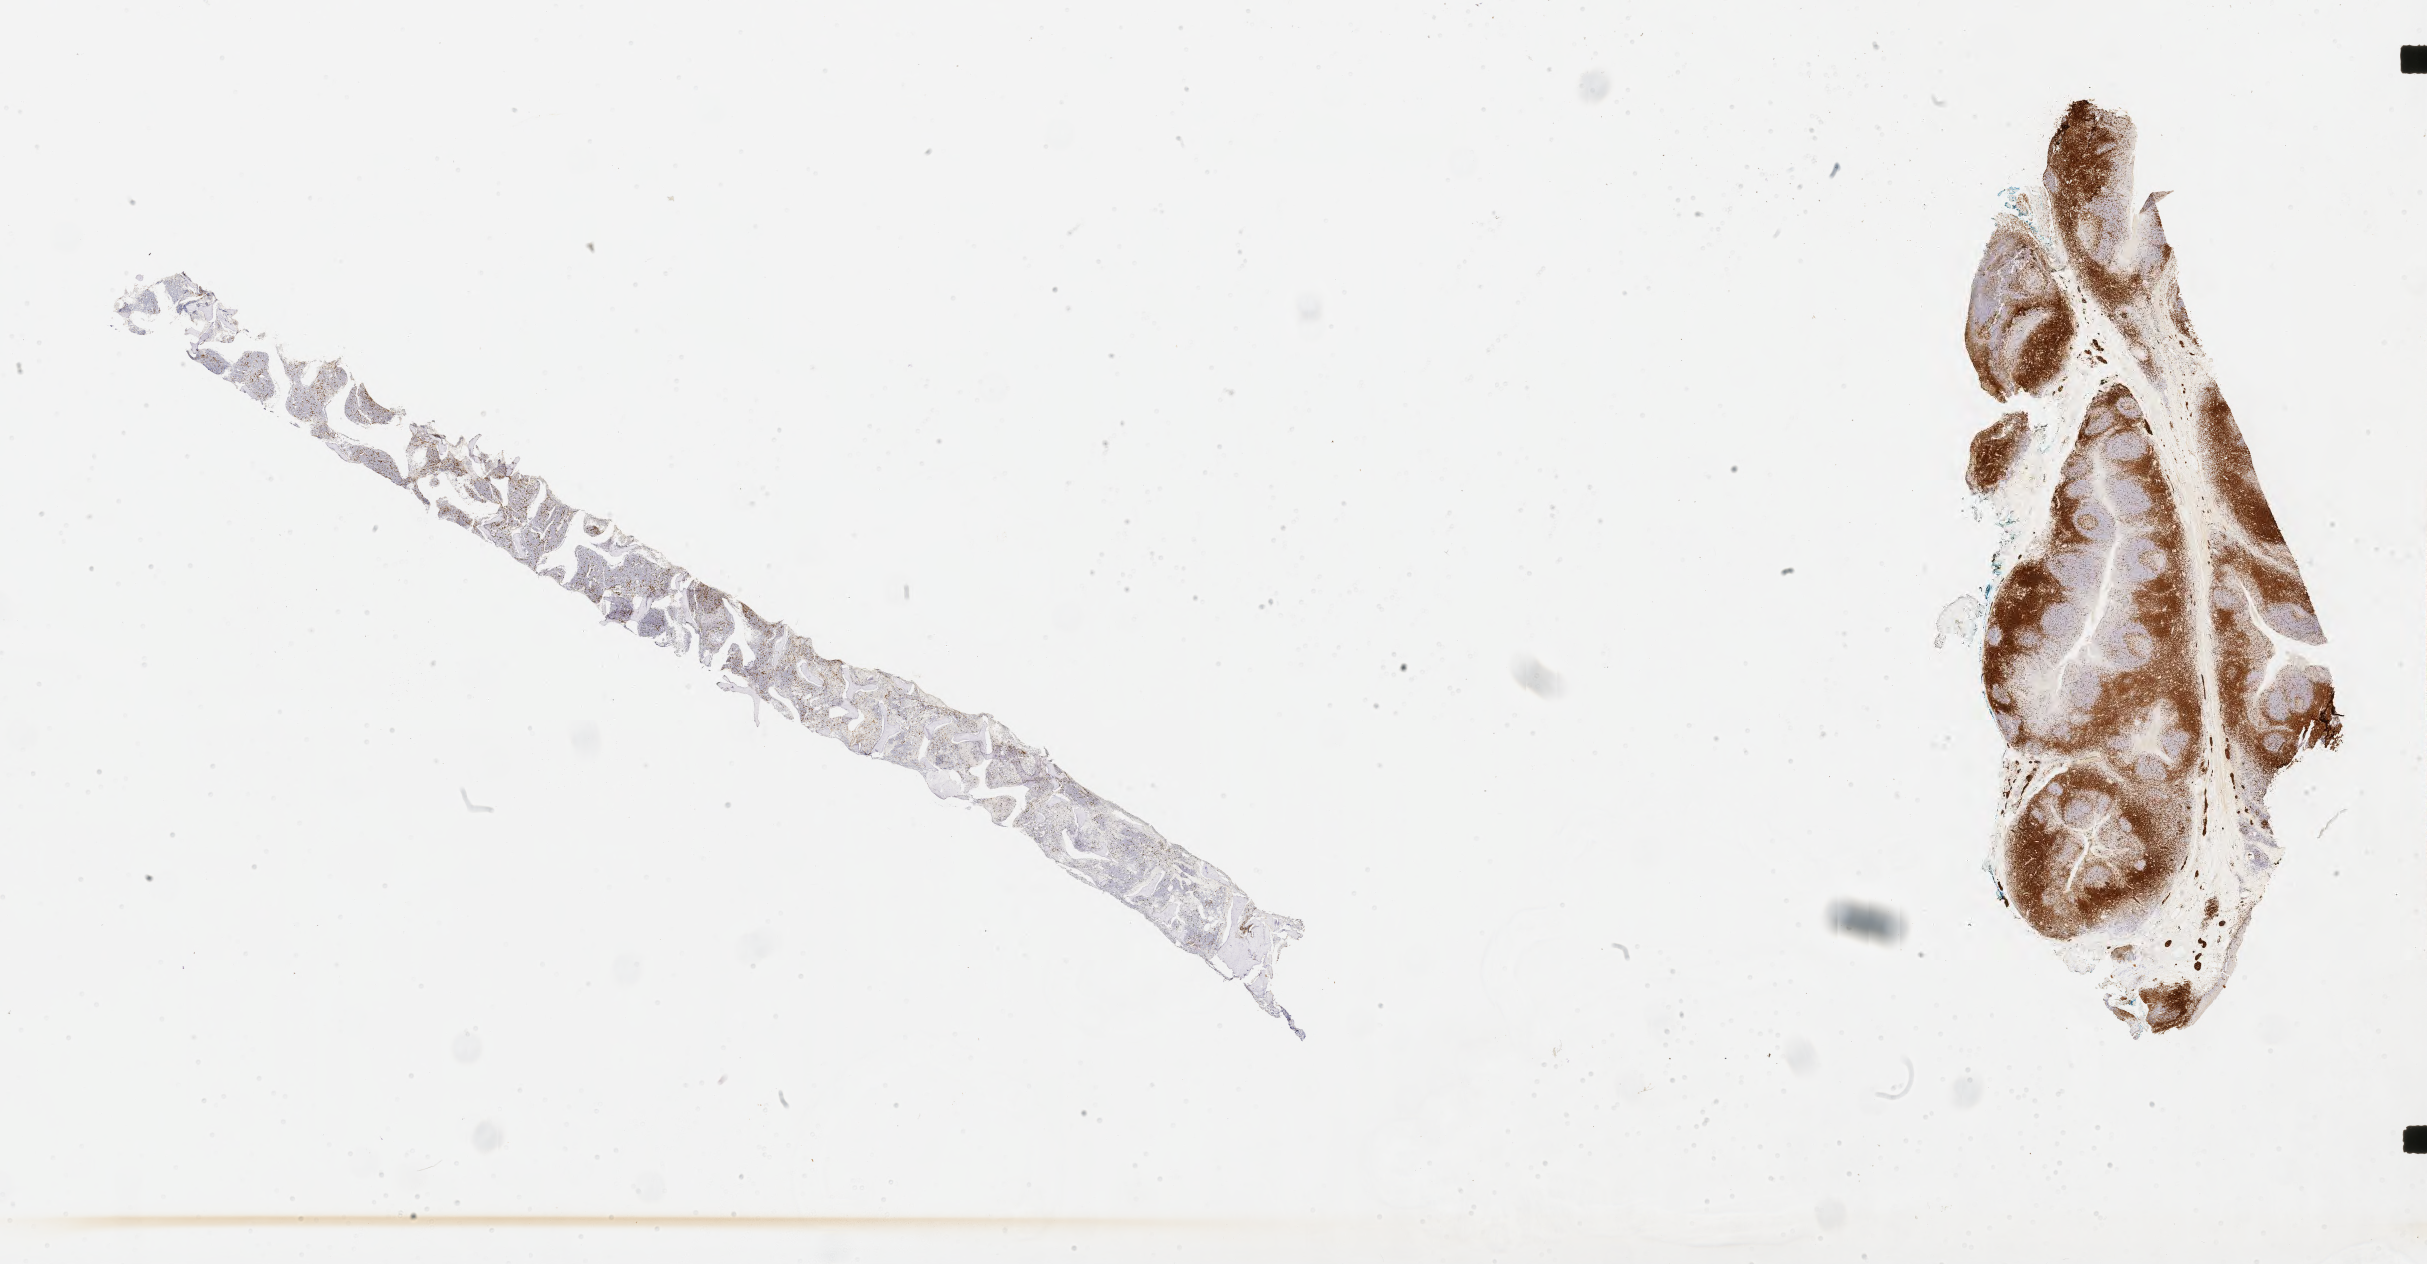
Whole-slide image, immunohistochemical stain for CD3, whole scanned area (about 39.2 x 20.4 mm) shown as a low-resolution overview; tumor tissue; site: bone marrow. Patient: male, 18 years old.
* histologic diagnosis: Burkitt lymphoma, NOS